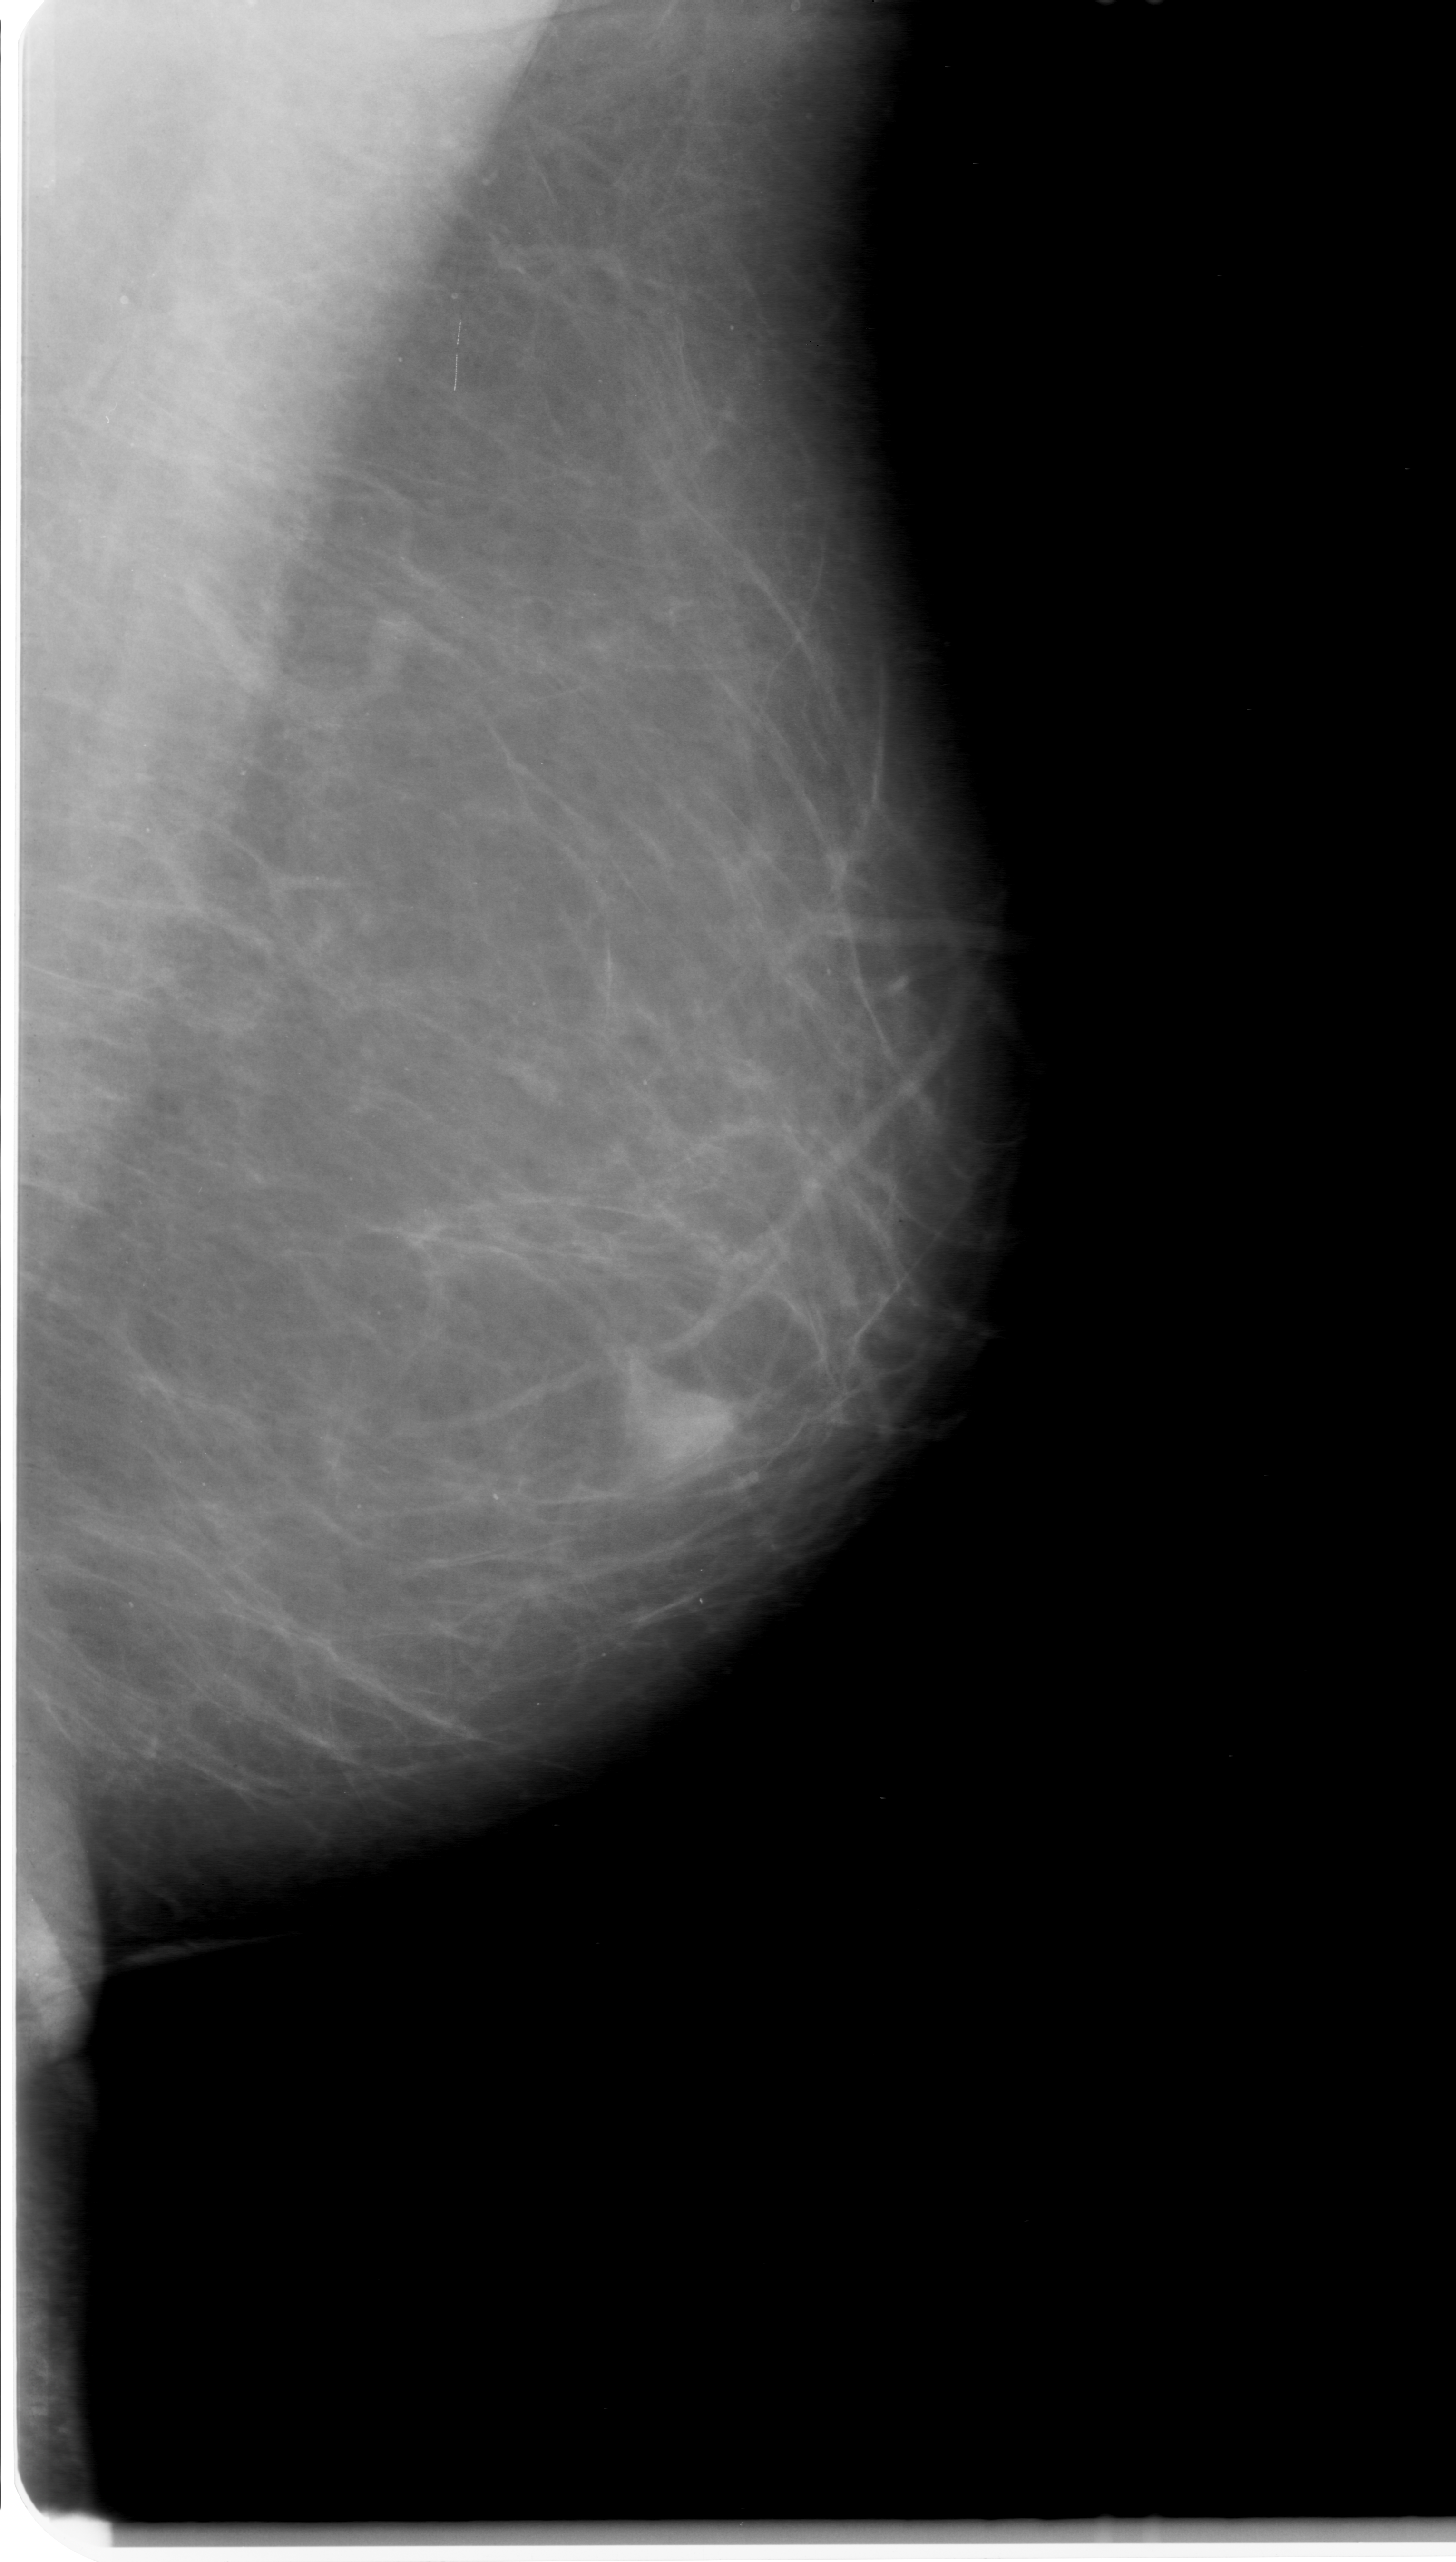
Digitized screen-film mammogram; left breast; MLO view; breast composition: almost entirely fatty (BI-RADS density category 1 of 4).
Marked abnormality: mass, shape irregular, margins obscured; BI-RADS assessment category 0 (incomplete: needs additional imaging); pathology result (as recorded, not read from the image): benign.